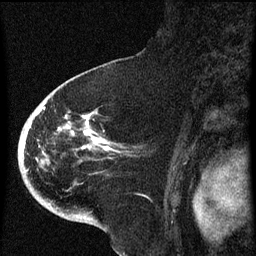
Breast MRI (dynamic contrast-enhanced), one sagittal slice; position 43 of 60 along the scan axis; dynamic contrast-enhanced series, image 2 of 4 at this slice position (ordered by acquisition); 1.5 T; TE 4.2 ms, TR 8 ms; 256 × 256 image matrix. Patient: female, 71 years.
Outlined on this slice (semi-automatically segmented with operator editing):
- analysis volume of interest (the breast-tissue region the enhancement analysis was run in; not a lesion): box from (x=32, y=86) to (x=131, y=205) px
- tumour enhancement mask (voxels above the 70 % enhancement threshold inside the analysis volume of interest): (x=40, y=108)–(x=120, y=153)